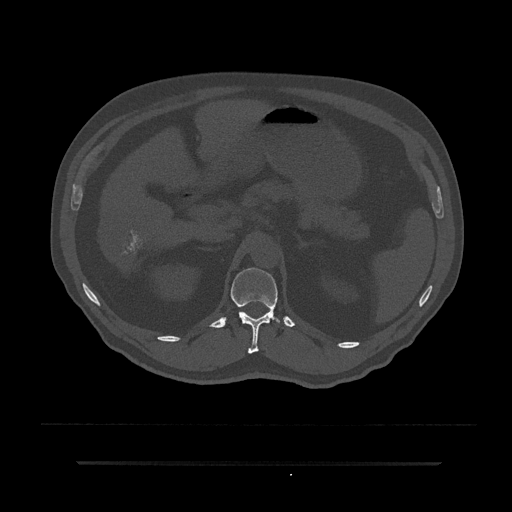
CT including the spine, one axial slice; slice 204 of 797 in the series (ordered by position); reconstruction kernel Br40s/3; bone window (W 1800 / L 400 HU); 0.5 mm slice thickness; 512 × 512 image matrix, field of view 464 × 464 mm. Patient: male, 59 years. From the clinical record (not read from this slice): primary cancer: bile ducts; vertebrae with lytic lesions (as recorded): T10.
Structures marked on this image (semi-automatically segmented with operator editing):
- T12 vertebra: bounding box <231,268,280,354> (left, top, right, bottom; pixels)